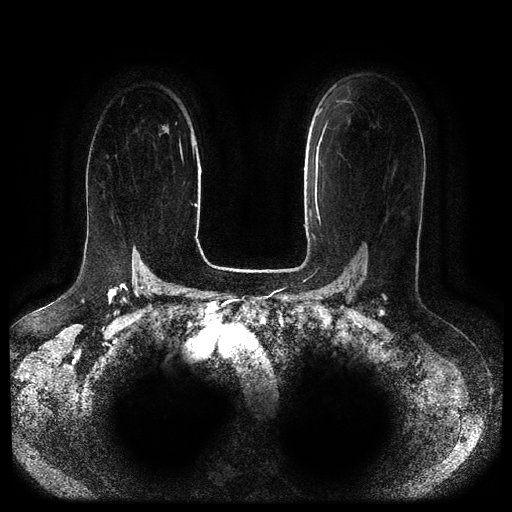
Breast MRI (dynamic contrast-enhanced, multi-phase), one axial slice. Position 67 of 116 along the scan axis. Dynamic contrast-enhanced series, time point 2 of 5 at this slice position (early post-contrast). 1.5 T. TE 2.6 ms, TR 5.3 ms. 2.1 mm slice thickness. 512 × 512 image matrix, field of view 360 × 360 mm. Patient: female, 65 years.
Outlined on this slice (semi-automatic segmentation, software-assisted and operator-edited):
- breast lesion (labelled benign in the annotation): bounding box <163,126,168,132> (left, top, right, bottom; pixels)